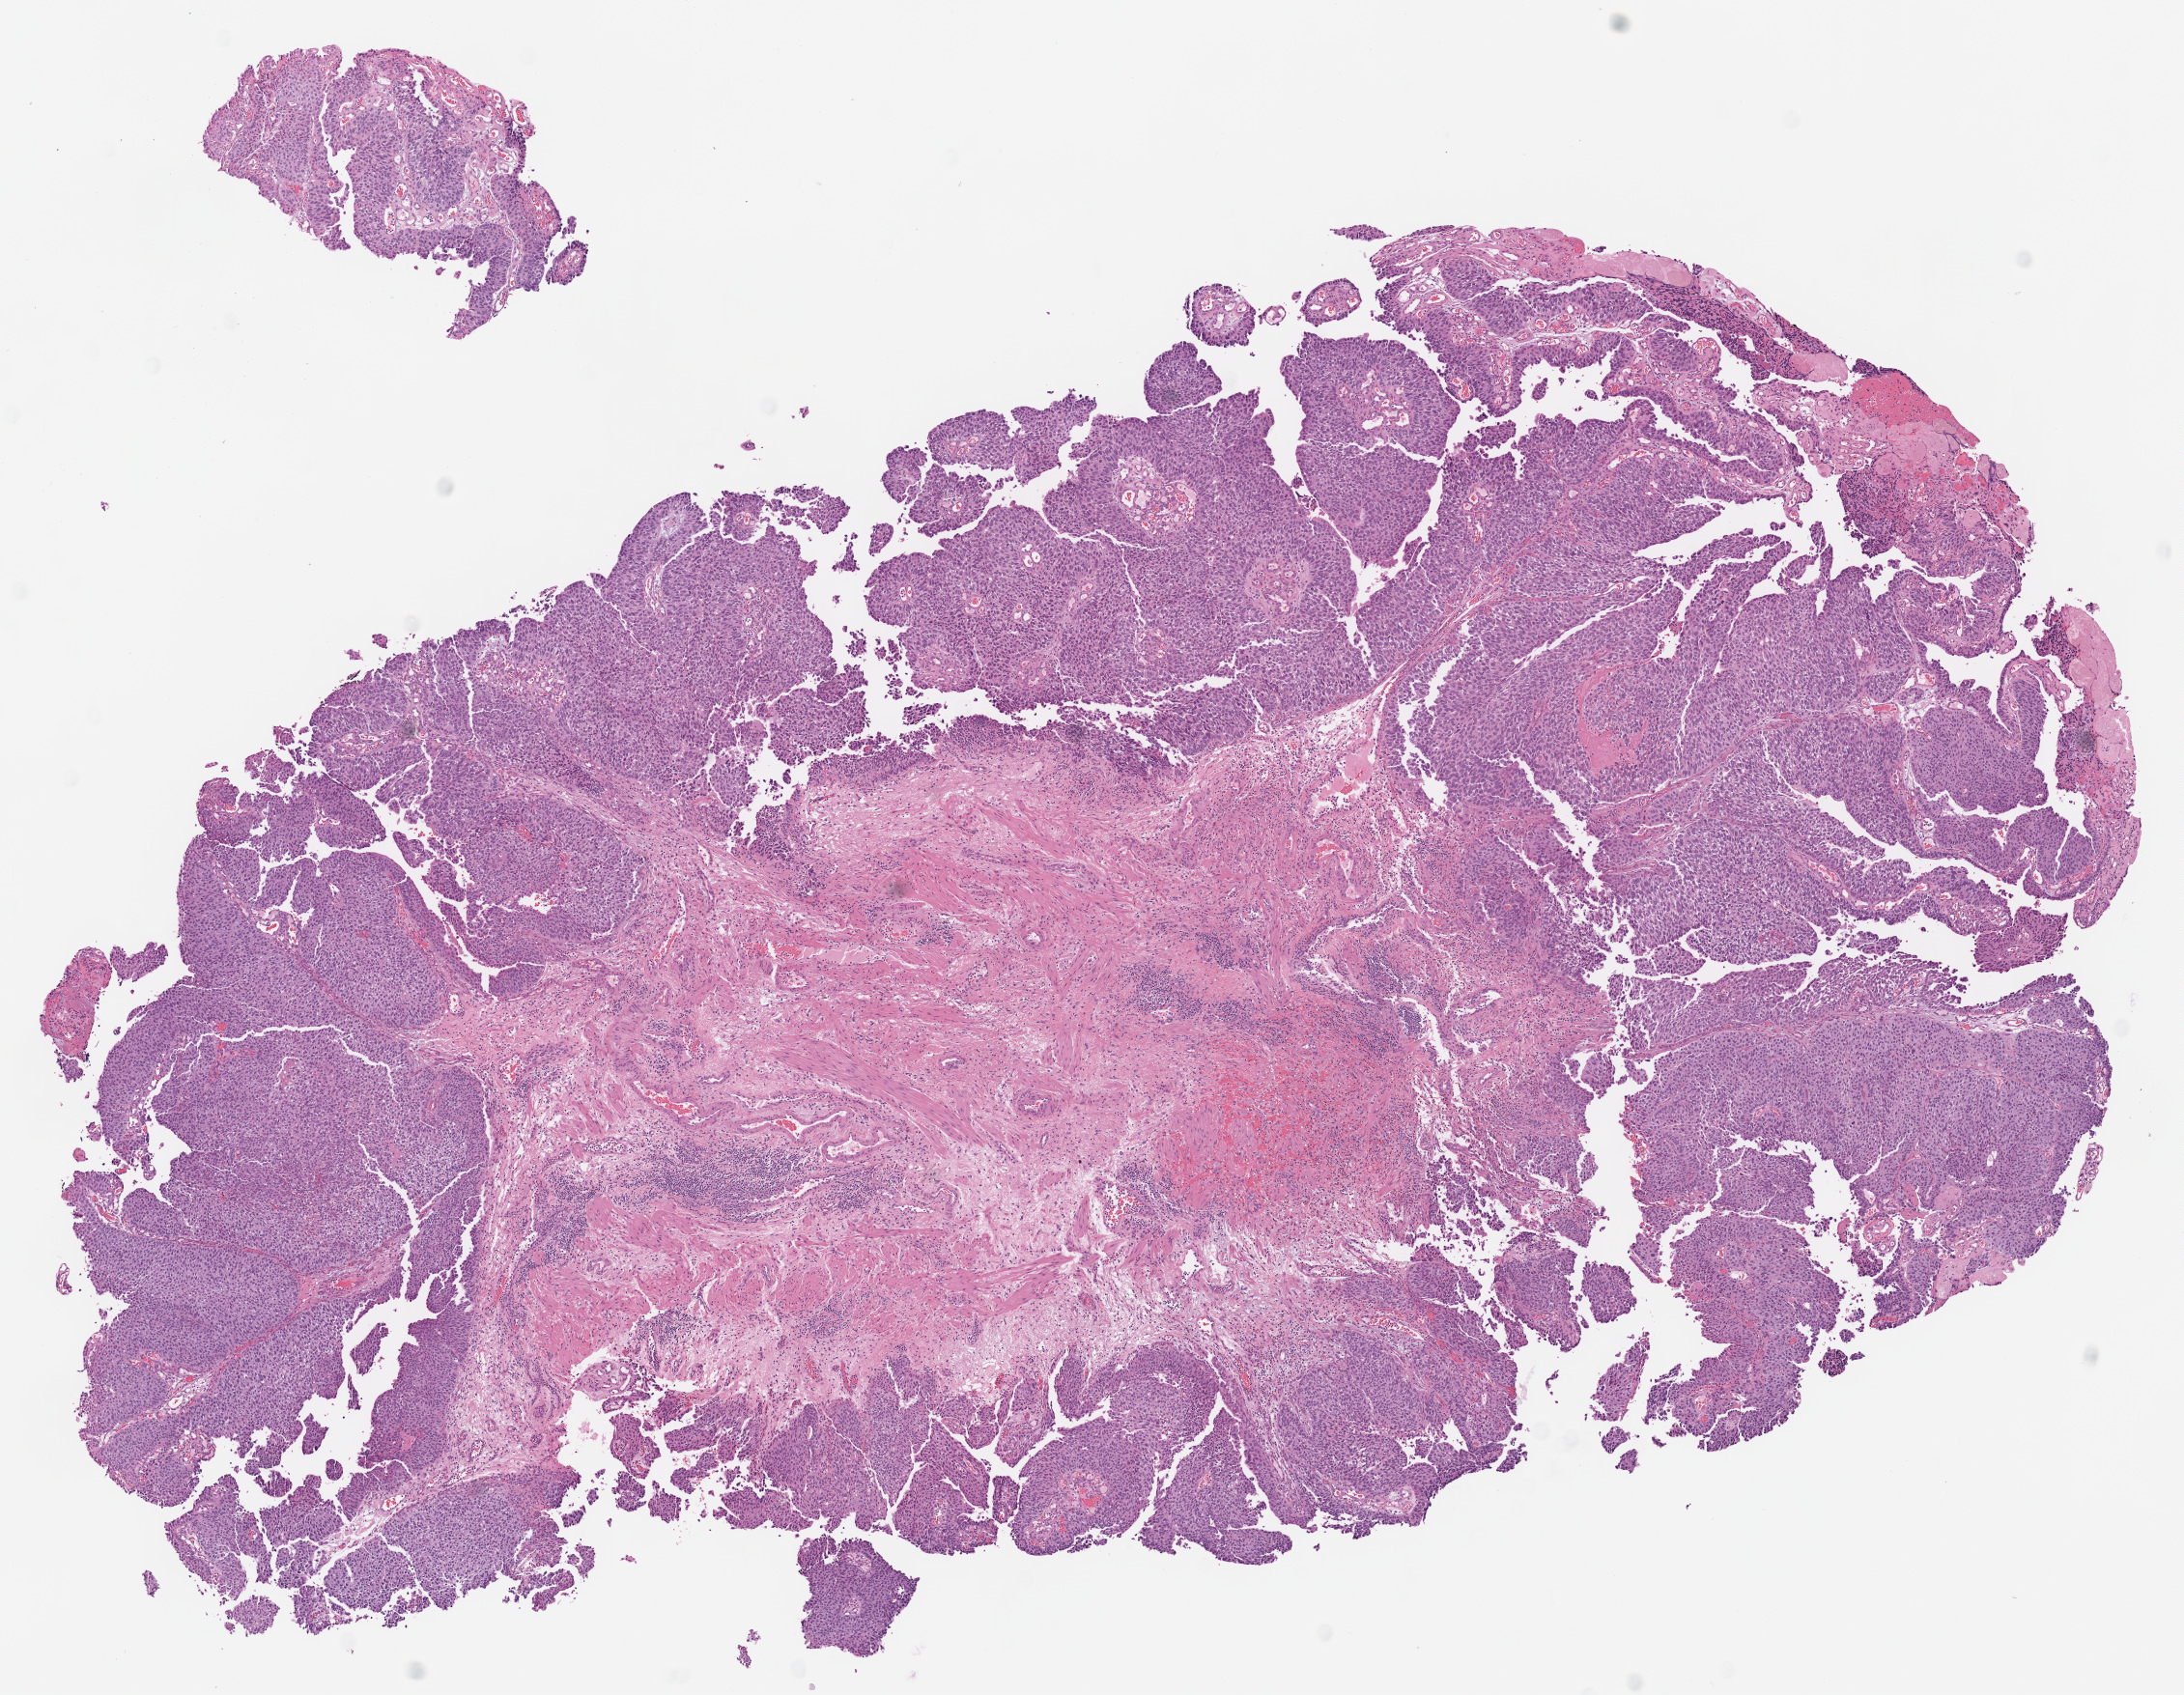
Whole-slide histology image, H&E-stained — a low-resolution overview of the entire scanned area, about 8.9 x 6.9 mm, formalin-fixed paraffin-embedded (FFPE) diagnostic section, sample: primary tumour, bladder. Patient: male, age at initial diagnosis 70 years. Histologic grade: high grade.
- pathologic diagnosis: Transitional cell carcinoma (dome of bladder)
- lymph nodes positive (case pathology): 0 of 2 examined
- AJCC pathologic stage: II (7th edition)